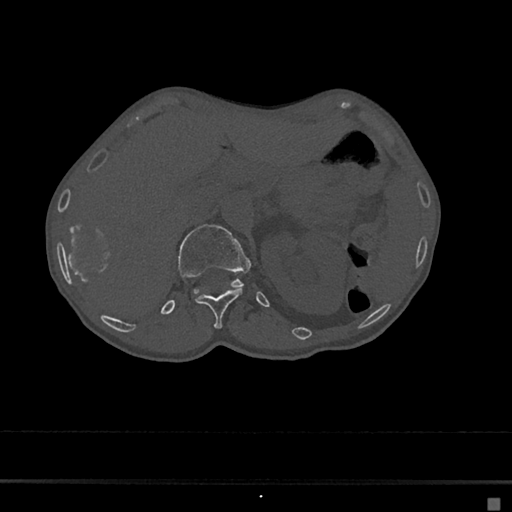
CT including the spine, one axial slice. Slice 101 of 797 in the series (ordered by position). Reconstruction kernel Br40s/3. 120 kVp. Bone window (W 1800 / L 400 HU). 512 × 512 image matrix, field of view 360 × 360 mm. Patient: female, 68 years. Case-level facts recorded for this patient, not image findings: primary cancer: renal.
Annotated regions visible in this slice (semi-automatically segmented with operator editing):
- L1 vertebra: box from (x=177, y=224) to (x=252, y=288) px
- T12 vertebra: (x=196, y=289)–(x=242, y=329)